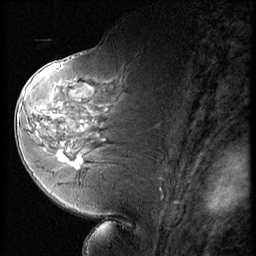
Breast MRI (dynamic contrast-enhanced), one sagittal slice; slice 31 of 56 in the series (ordered by position); 3 images stored at this slice position (order not interpretable as contrast timing); 1.5 T; TE 4.2 ms, TR 9 ms; 2.5 mm slice thickness; 256 × 256 image matrix, field of view 180 × 180 mm. Female patient, age 58 years. Case-level facts recorded for this patient, not image findings: setting: breast cancer imaged before/during neoadjuvant chemotherapy; receptor status: HR-positive, HER2-negative.
Structures marked on this image (semi-automatic segmentation, software-assisted and operator-edited):
- analysis volume of interest (the breast-tissue region the enhancement analysis was run in; not a lesion): bounding box [x1, y1, x2, y2] px = [47, 136, 88, 178]
- tumour enhancement mask (voxels above the 140 % enhancement threshold inside the analysis volume of interest): [57, 150, 82, 166]